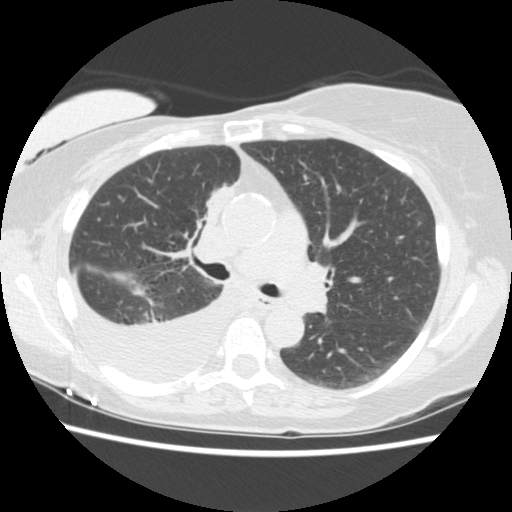
Low-dose screening chest CT, one axial slice; position 92 of 157 along the scan axis; lung window (W 1500 / L -600 HU); 2.5 mm slice thickness; 512 × 512 image matrix.
Annotated regions visible in this slice (expert manual segmentation):
- lesion 1 (tumor, upper lobe of right lung): box from (x=205, y=185) to (x=234, y=225) px